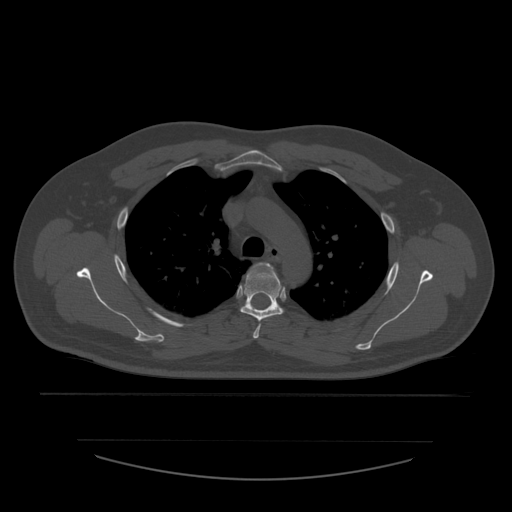
CT including the spine, one axial slice; position 419 of 532 along the scan axis; reconstruction kernel STANDARD; 120 kVp; bone window (W 1800 / L 400 HU); 1.25 mm slice thickness; 512 × 512 image matrix, field of view 441 × 441 mm. Patient age 44 years. From the clinical record (not read from this slice): primary cancer: soft tissue sarcoma.
Outlined on this slice (semi-automatic segmentation, software-assisted and operator-edited):
- T3 vertebra: box from (x=253, y=263) to (x=274, y=339) px
- T4 vertebra: (x=241, y=266)–(x=283, y=320)